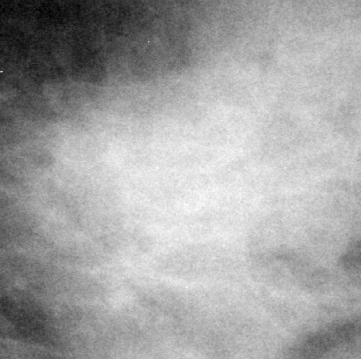
Region of interest cut from a scanned film mammogram (one marked finding), left breast, MLO view.
Finding: mass, shape lobulated, margins circumscribed / ill defined; BI-RADS assessment category 4; pathology (as recorded): benign.